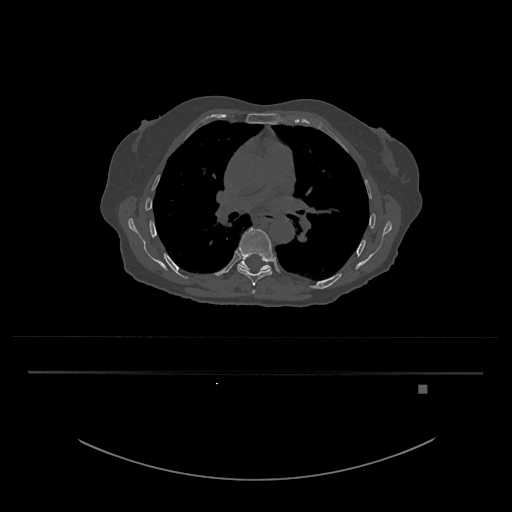
CT including the spine, one axial slice; bone window (W 1800 / L 400 HU); 0.5 mm slice thickness; 512 × 512 image matrix, field of view 500 × 500 mm. Female patient, age 57 years. From the clinical record (not read from this slice): primary cancer: cervical.
Outlined on this slice (semi-automatically segmented with operator editing):
- T8 vertebra: box from (x=236, y=227) to (x=275, y=286) px
- T9 vertebra: (x=238, y=257)–(x=271, y=272)